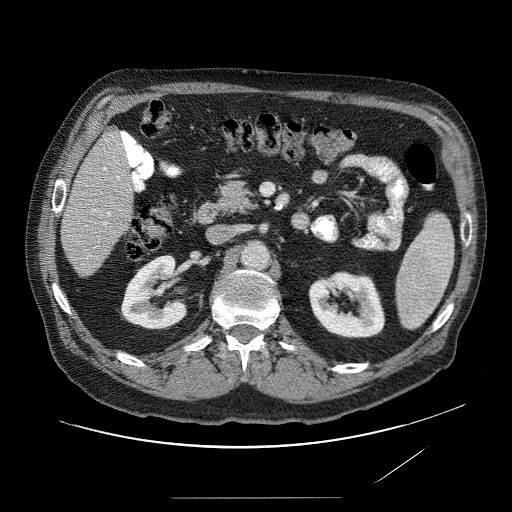
Contrast-enhanced abdominal CT (liver protocol), one axial slice. Position 22 of 89 along the scan axis. Reconstruction kernel STANDARD. Soft-tissue window (W 400 / L 40 HU). 512 × 512 image matrix, field of view 420 × 420 mm. From the clinical record (not read from this slice): diagnosis: hepatocellular carcinoma (patient treated with transarterial chemoembolisation; whether this scan precedes or follows treatment is not stated here); TNM stage (as recorded): Stage-IVA; Child-Pugh class: A.
Annotated regions visible in this slice (semi-automatic segmentation, software-assisted and operator-edited):
- liver parenchyma outside the tumour (the mass and vessels are separate outlines, so this box may not span the whole liver): bounding box <60,122,140,280> (left, top, right, bottom; pixels)
- liver vessels: <92,130,127,238>